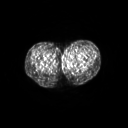
FDG PET of an extremity soft-tissue mass (from a PET/CT study), one axial slice; slice 37 of 267 in the series (ordered by position); 3.27 mm slice thickness; 128 × 128 image matrix, field of view 600 × 600 mm. Patient: female, 24 years. From the clinical record (not read from this slice): histological type: leiomyosarcoma; grade: high; site of the primary tumour: groin.
Annotated regions visible in this slice (expert contour drawn on MRI and transferred to this co-registered scan by the dataset authors):
- gross tumour volume including surrounding oedema: bounding box (x1, y1, x2, y2) in pixels: (61, 54, 70, 63)